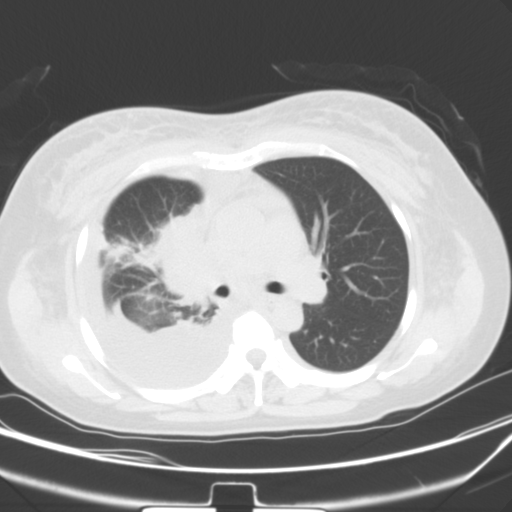
Chest CT, one axial slice. Slice 32 of 54 in the series (ordered by position). 120 kVp. Lung window (W 1500 / L -600 HU). 512 × 512 image matrix, field of view 347 × 347 mm. Patient: female, 36 years. Case-level facts recorded for this patient, not image findings: clinical TNM (as recorded): T1b N2 M0; histopathological grade: G3.
Outlined on this slice (bounding box drawn by a radiologist):
- lung tumour (recorded histology: adenocarcinoma): box from (x=151, y=207) to (x=223, y=300) px